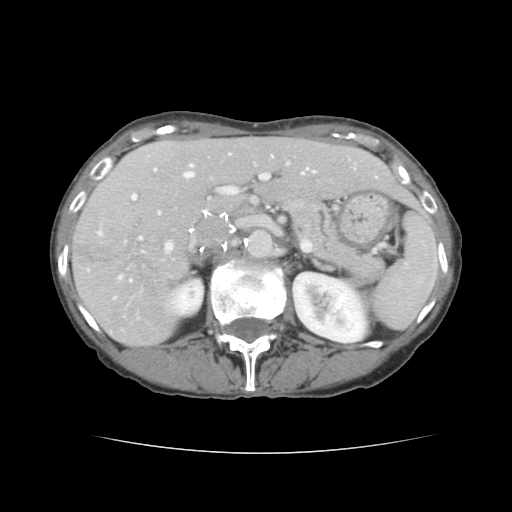
Contrast-enhanced abdominal CT, one axial slice. Position 83 of 136 along the scan axis. Intravenous contrast given. Soft-tissue window (W 400 / L 40 HU). 2.5 mm slice thickness. 512 × 512 image matrix. Female patient, age 77 years. From the clinical record (not read from this slice): diagnosis: colorectal cancer liver metastases, imaged before liver resection; multiple liver metastases: yes; largest metastasis: 3 cm; disease in both lobes: no.
Structures marked on this image (outlined manually by an expert reader):
- hepatic veins: box from (x=140, y=153) to (x=308, y=239) px
- liver: (x=73, y=137)–(x=415, y=346)
- planned liver remnant (the part of the liver to remain after resection): (x=154, y=137)–(x=414, y=211)
- portal vein (with intrahepatic branches): (x=98, y=162)–(x=355, y=281)